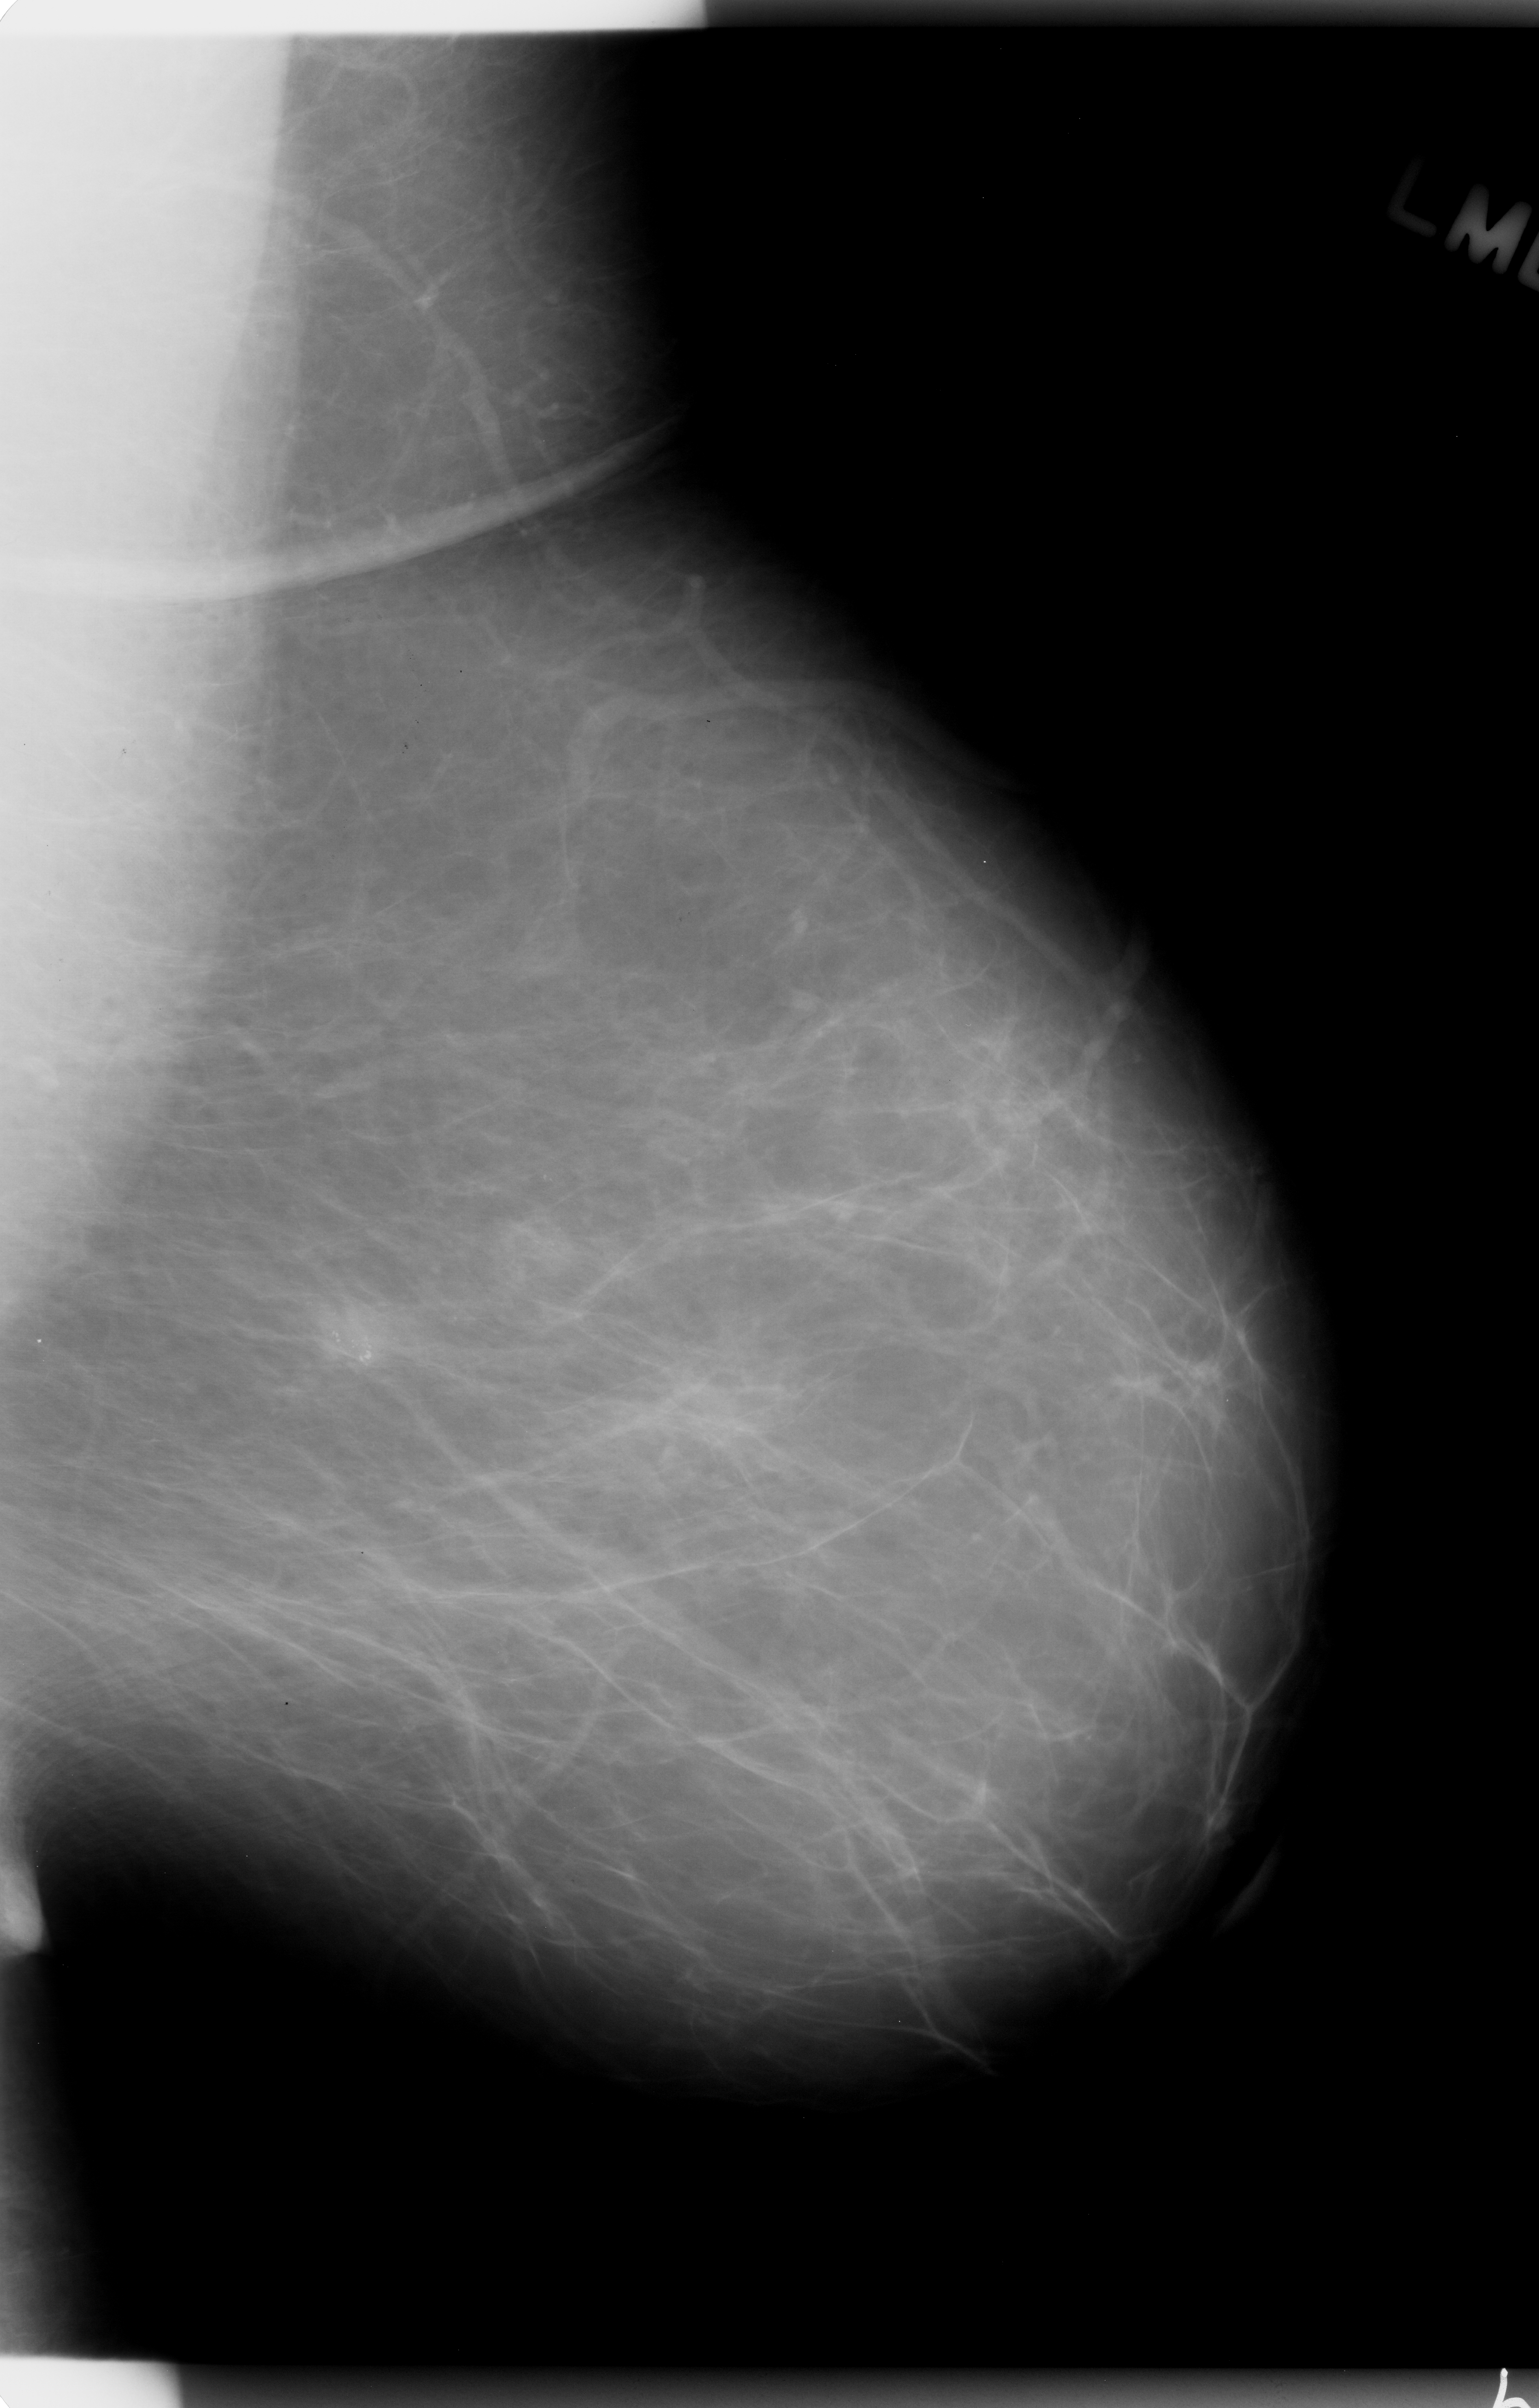
Scanned film-screen mammogram; left breast; mediolateral oblique (MLO) view; 1539 × 2408 image matrix.
Expert-marked regions of interest on this film, with their recorded descriptors:
- calcifications, morphology pleomorphic, distribution clustered; BI-RADS assessment category 4; subtlety rating 4 on a 1 (subtle) to 5 (obvious) scale; pathology result (as recorded, not read from the image): malignant: bounding box <250,1132,668,1442> (left, top, right, bottom; pixels)